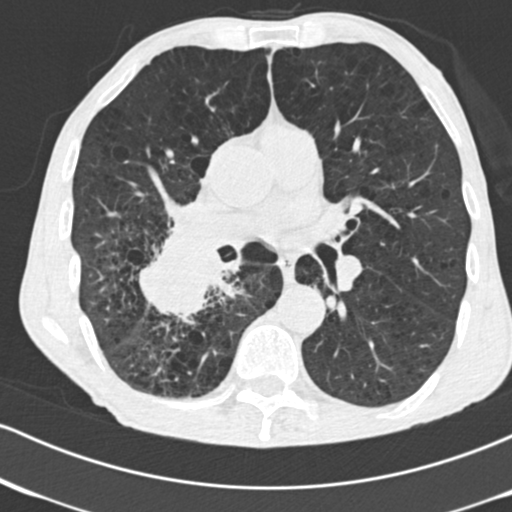
Low-dose screening chest CT, axial slice, second screening round (one year after baseline), lung window (W 1500 / L -600 HU), 2 mm slice thickness, 120 kVp. Male, age 64 years at enrolment. Current smoker at enrolment.
- Expert-annotated lung lesion, bounding box [x1, y1, x2, y2] px = [130, 229, 240, 331].
- Reader record for this screening exam (exam-level; its link to the box is not recorded): non-calcified nodule or mass ≥4 mm, 52 × 37 mm, spiculated (stellate) margins, soft tissue attenuation, pre-existing on the prior screen: no.
- Participant outcome: lung cancer diagnosed 28 days after this screen — adenocarcinoma, NOS, right lower lobe, stage IV (AJCC 6th edition), 60 mm at pathology.